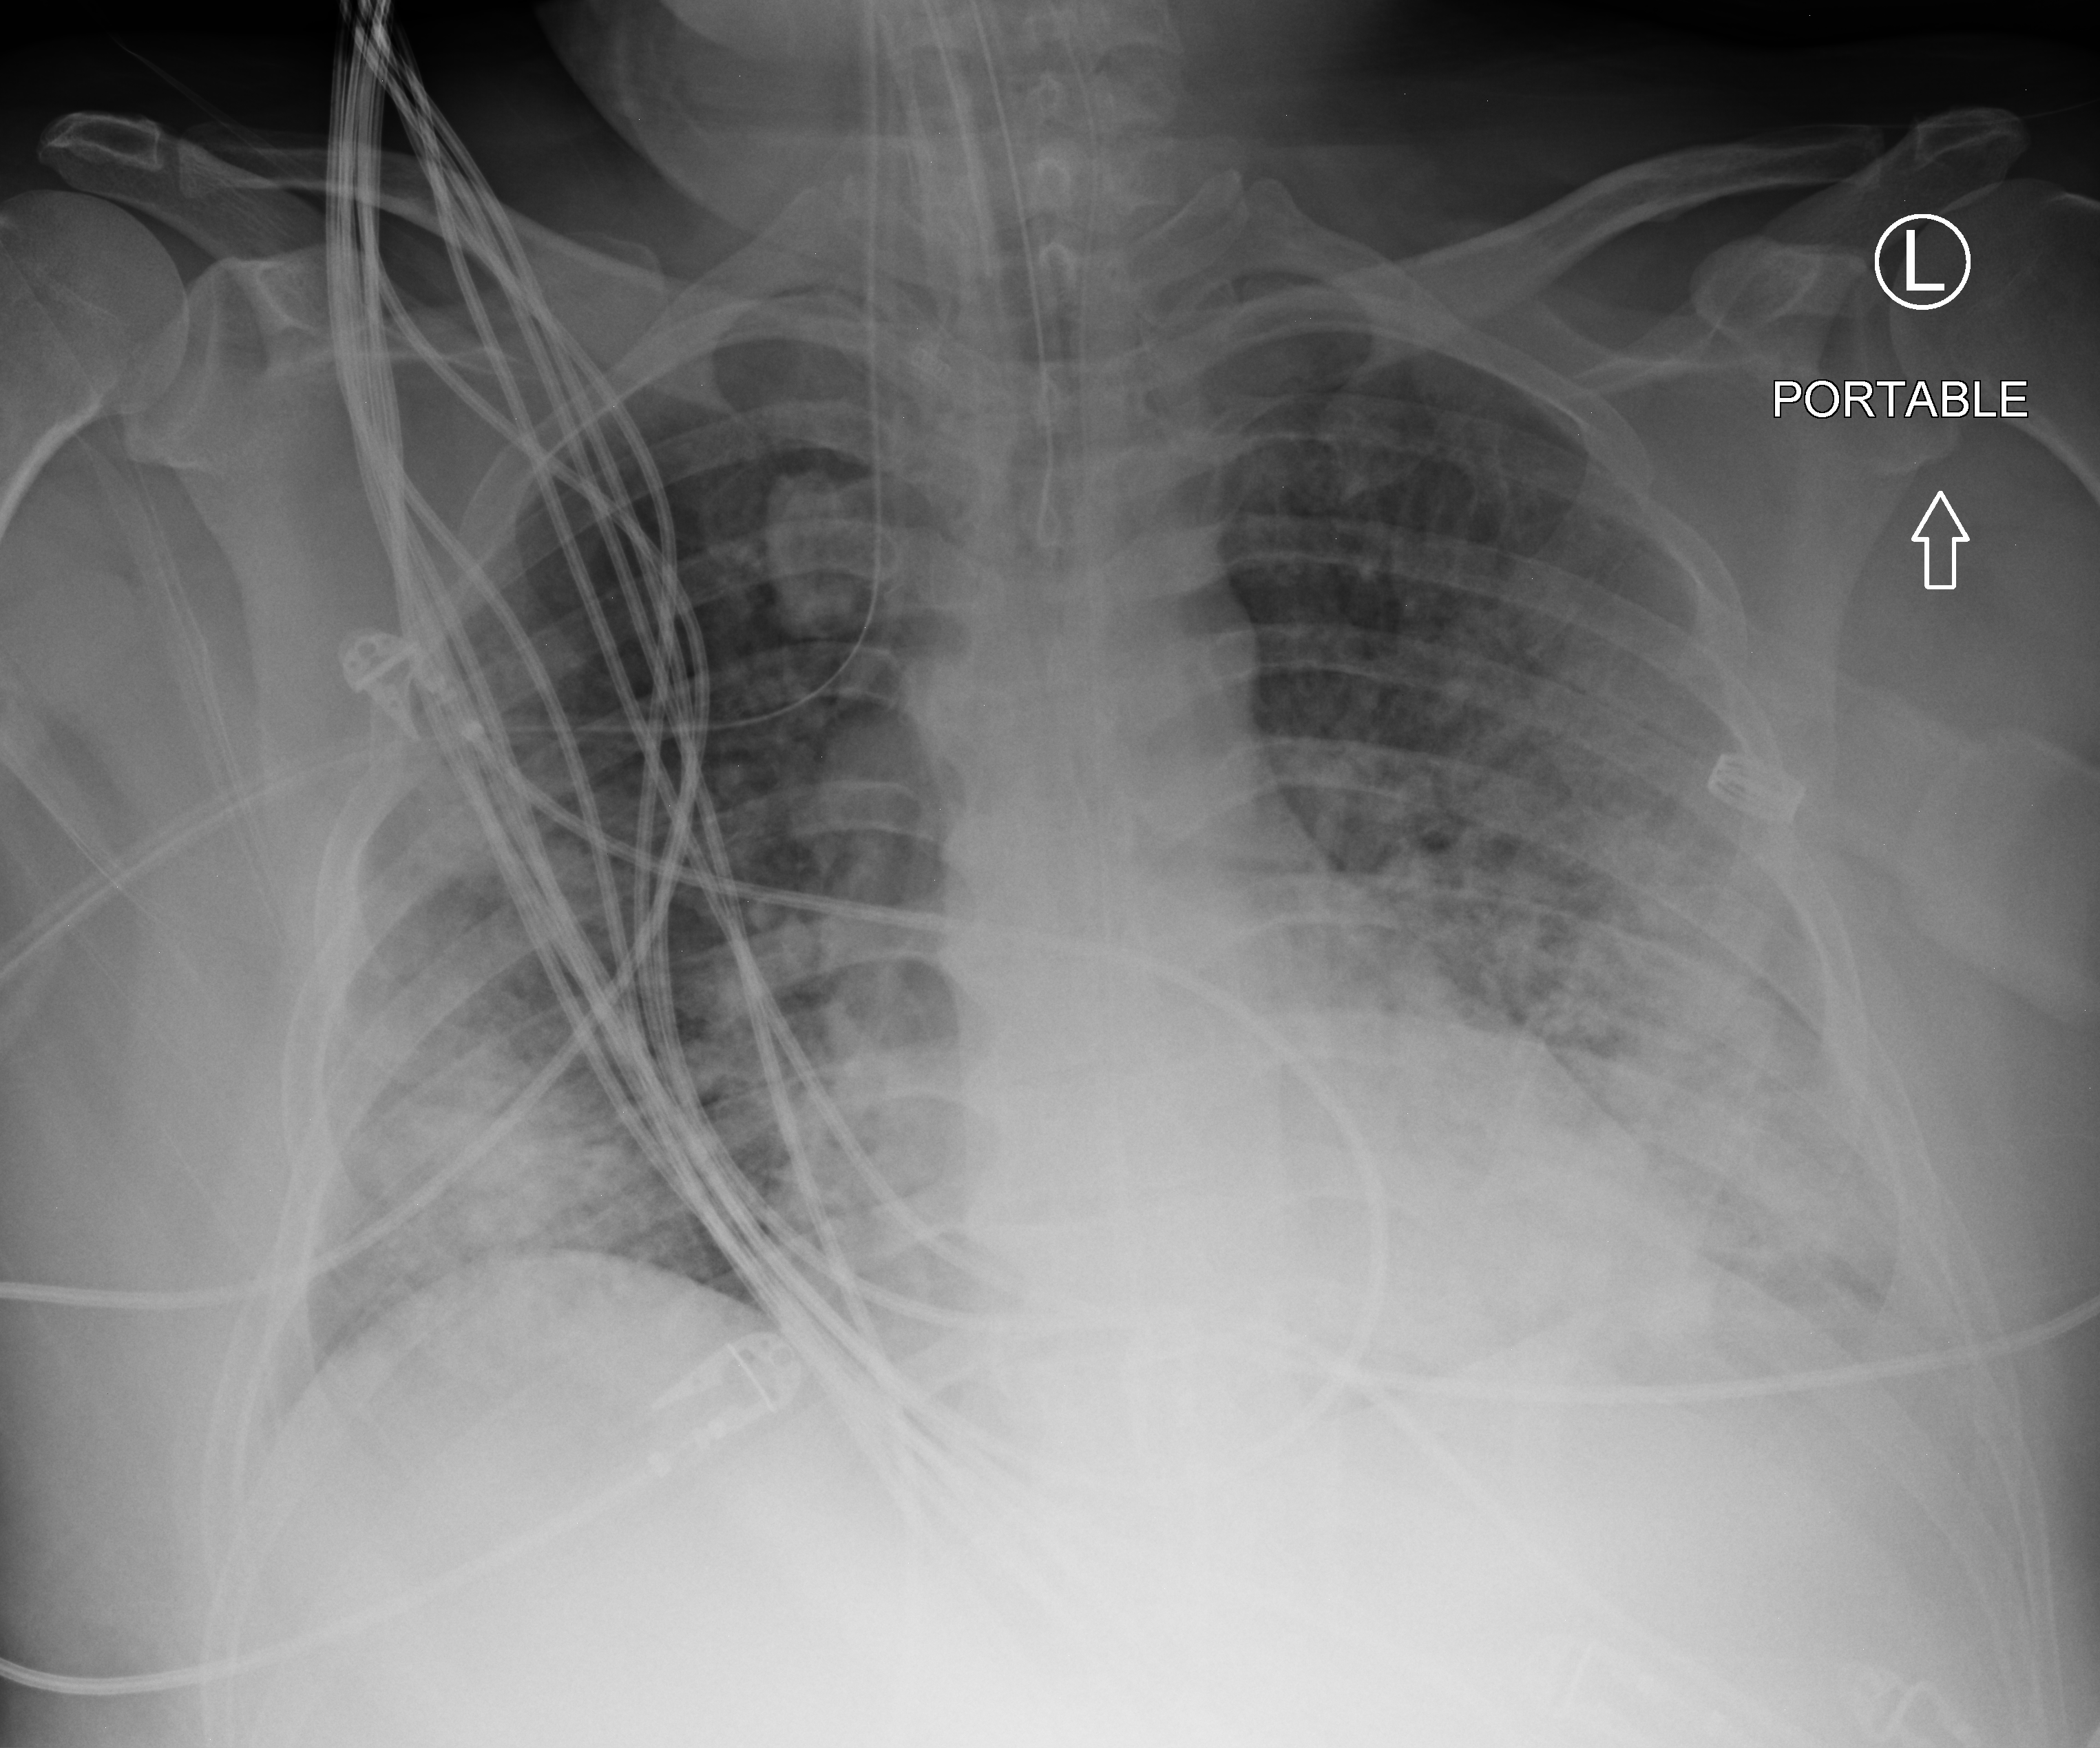
Bedside chest radiograph (computed radiography); anteroposterior (AP) projection. Patient hospitalised with COVID-19; male, aged 18–59 years.
Admission-level facts for this patient (not findings on this image; timing relative to this image not recorded): other chronic lung disease (admission record): no.